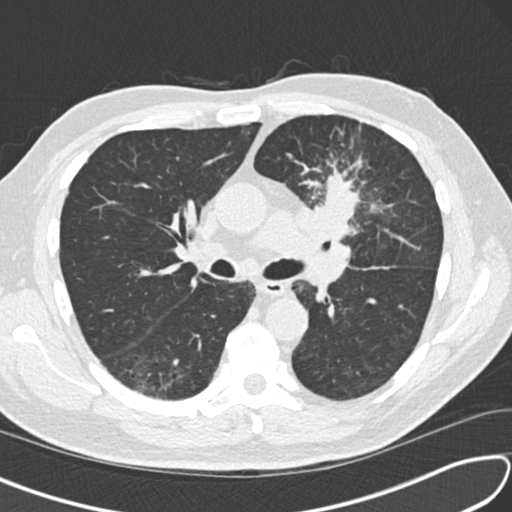
Low-dose screening chest CT, one axial slice. Slice 94 of 156 in the series (ordered by position). 120 kVp. Lung window (W 1500 / L -600 HU). 2 mm slice thickness. 512 × 512 image matrix.
Annotated regions visible in this slice (expert manual segmentation):
- lesion 1 (tumor, upper lobe of left lung): bounding box [x1, y1, x2, y2] px = [312, 176, 358, 240]